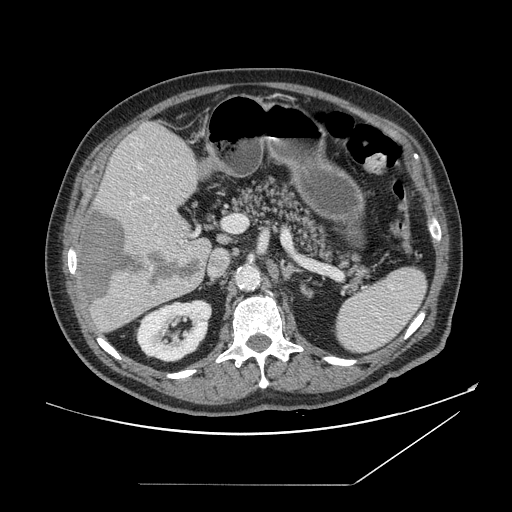
Contrast-enhanced abdominal CT, one axial slice; position 87 of 166 along the scan axis; 120 kVp; soft-tissue window (W 400 / L 40 HU); 512 × 512 image matrix. Male patient, age 80 years. From the clinical record (not read from this slice): diagnosis: colorectal cancer liver metastases, imaged before liver resection; multiple liver metastases: no; largest metastasis: 2.2 cm; disease in both lobes: no.
Outlined on this slice (manually delineated by an expert):
- hepatic veins: bounding box [x1, y1, x2, y2] px = [138, 165, 148, 200]
- liver: [78, 123, 211, 333]
- planned liver remnant (the part of the liver to remain after resection): [99, 123, 208, 245]
- portal vein (with intrahepatic branches): [131, 193, 231, 243]
- liver metastasis: [82, 210, 205, 304]